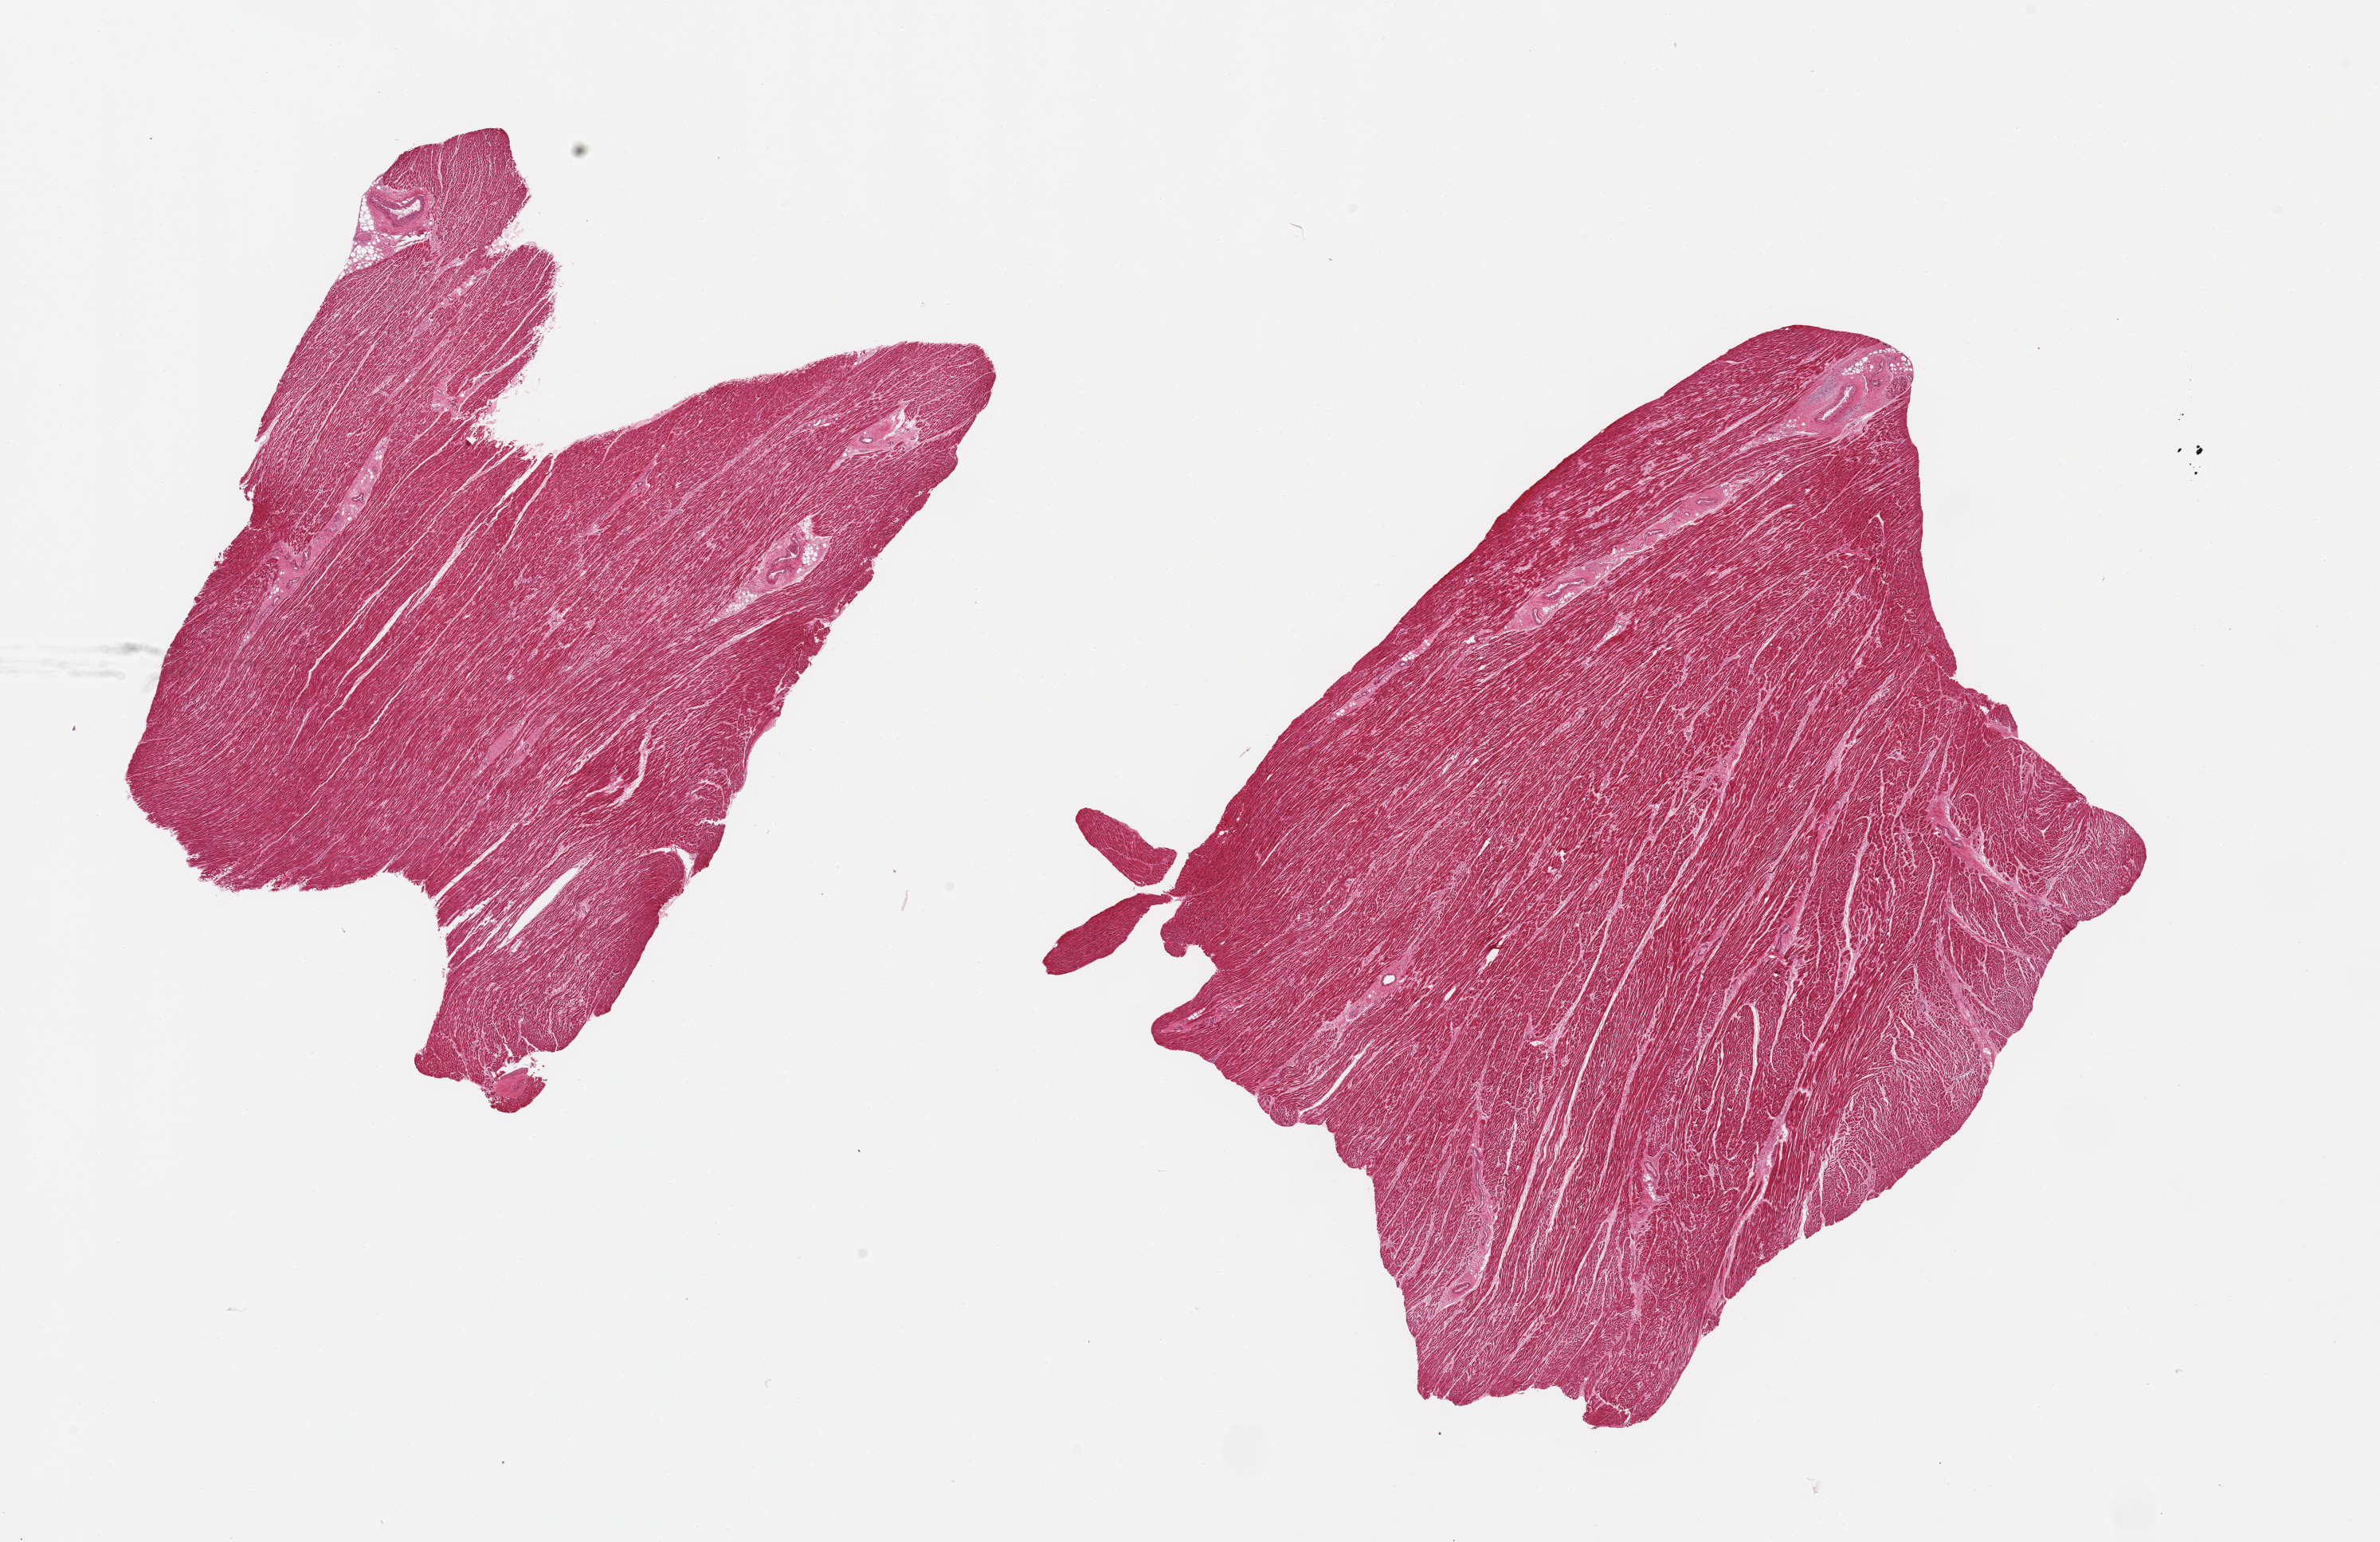
Whole-slide image, haematoxylin and eosin stain, brightfield, low-resolution overview of the scanned area, about 23.6 x 15.3 mm. PAXgene-fixed, paraffin-embedded tissue. Section of heart (target tissue). Tissue donor sample. Donor: male.
Reviewer comment on this tissue sample: 2 pieces, moderate chronic ischemic changes/interstitial fibrosis.